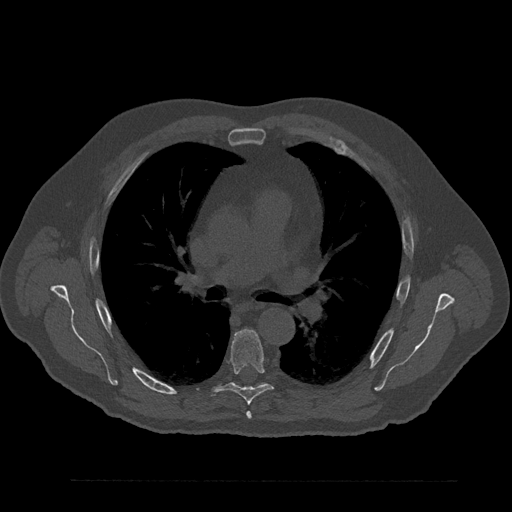
CT including the spine, one axial slice. Reconstruction kernel Br40s/3. 120 kVp. Bone window (W 1800 / L 400 HU). 0.5 mm slice thickness. 512 × 512 image matrix, field of view 430 × 430 mm. Patient: male, 61 years. From the clinical record (not read from this slice): primary cancer: prostate.
Annotated regions visible in this slice (semi-automatic segmentation, software-assisted and operator-edited):
- T5 vertebra: bounding box <246,412,252,419> (left, top, right, bottom; pixels)
- T6 vertebra: <210,329,273,405>